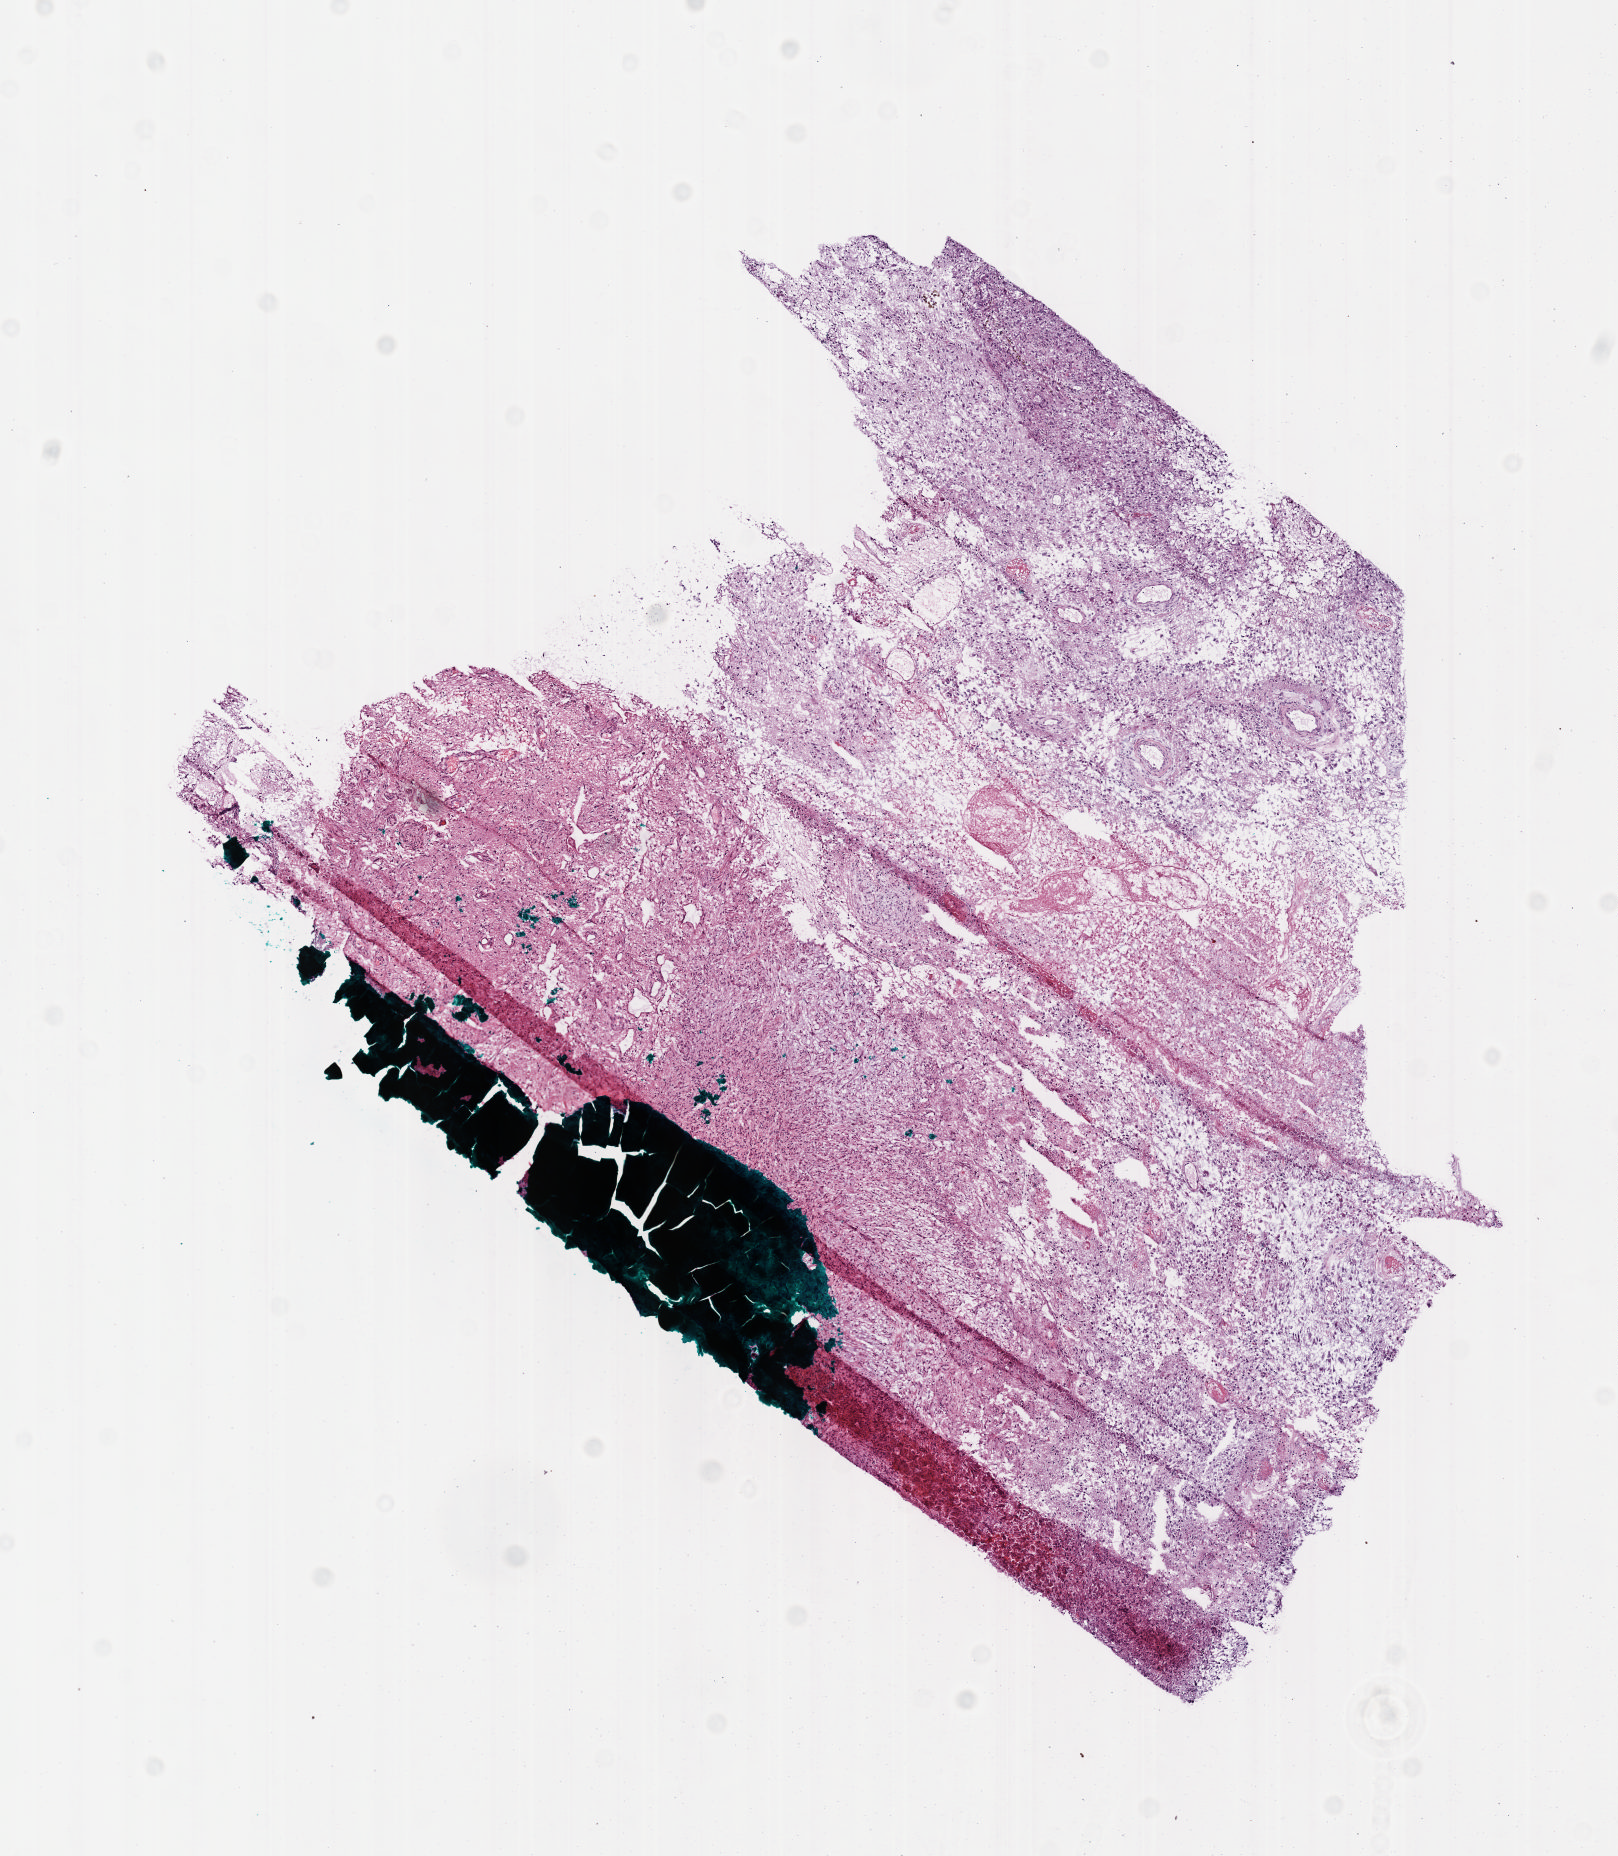
Digitized H&E-stained tissue section (whole slide) — low-resolution overview of the scanned area, about 6.5 x 7.5 mm (acquisition: 40x scan); frozen section; primary tumour sample from the brain. Patient: male, age at initial diagnosis 43 years. Composition of this section per pathologist review: tumour cells 85%, tumour nuclei 85%, normal cells 0%, stromal cells 10%, necrosis 5%.
Pathologic diagnosis: Glioblastoma.